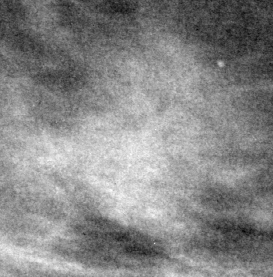
Region of interest cut from a scanned film mammogram (one marked finding), left breast, MLO view, BI-RADS breast density category 1 (scale 1–4).
Mass, shape irregular, margins spiculated; BI-RADS assessment category 4; pathology (as recorded): malignant.